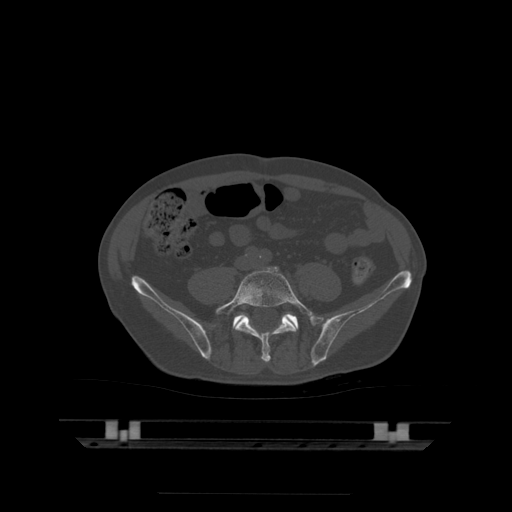
CT including the spine, one axial slice. Position 71 of 522 along the scan axis. Bone window (W 1800 / L 400 HU). 512 × 512 image matrix, field of view 436 × 436 mm. Patient age 68 years. Case-level facts recorded for this patient, not image findings: primary cancer: urothelial.
Structures marked on this image (semi-automatic segmentation, software-assisted and operator-edited):
- L5 vertebra: box from (x=216, y=267) to (x=314, y=363) px